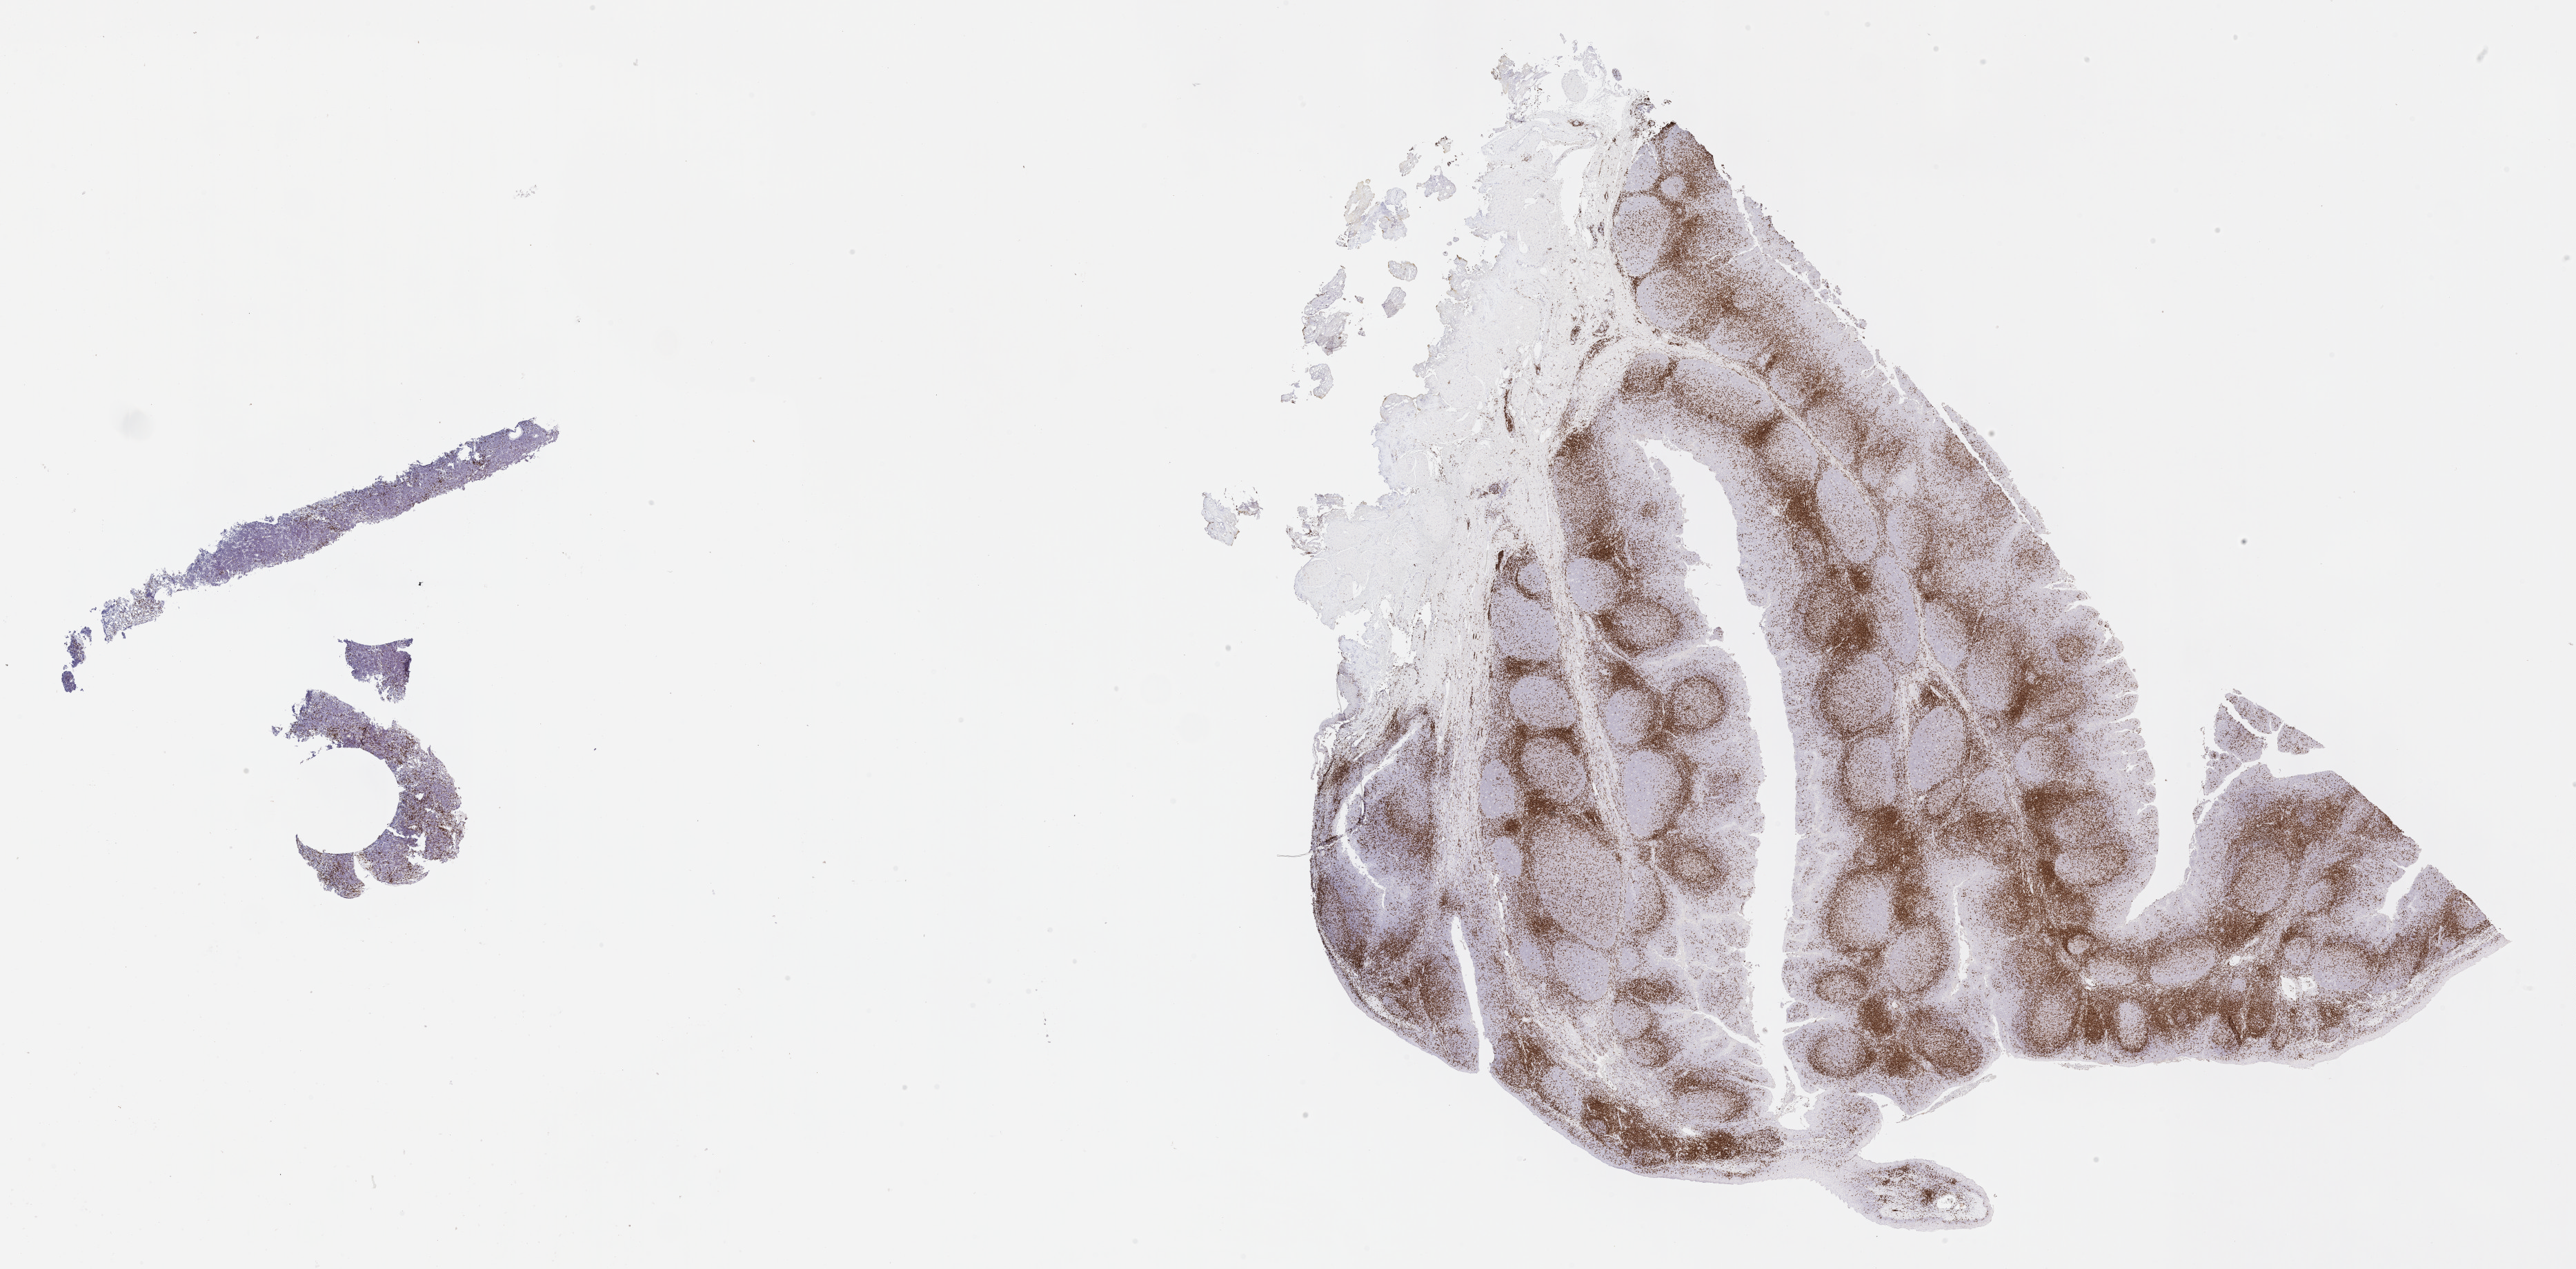
Whole-slide image, immunohistochemical stain for CD3 — low-resolution overview of the scanned area, about 30.2 x 14.9 mm. Specimen: tumor tissue. Site: ovary. Patient: female, age 10 years.
Histologic diagnosis: Burkitt lymphoma, NOS.